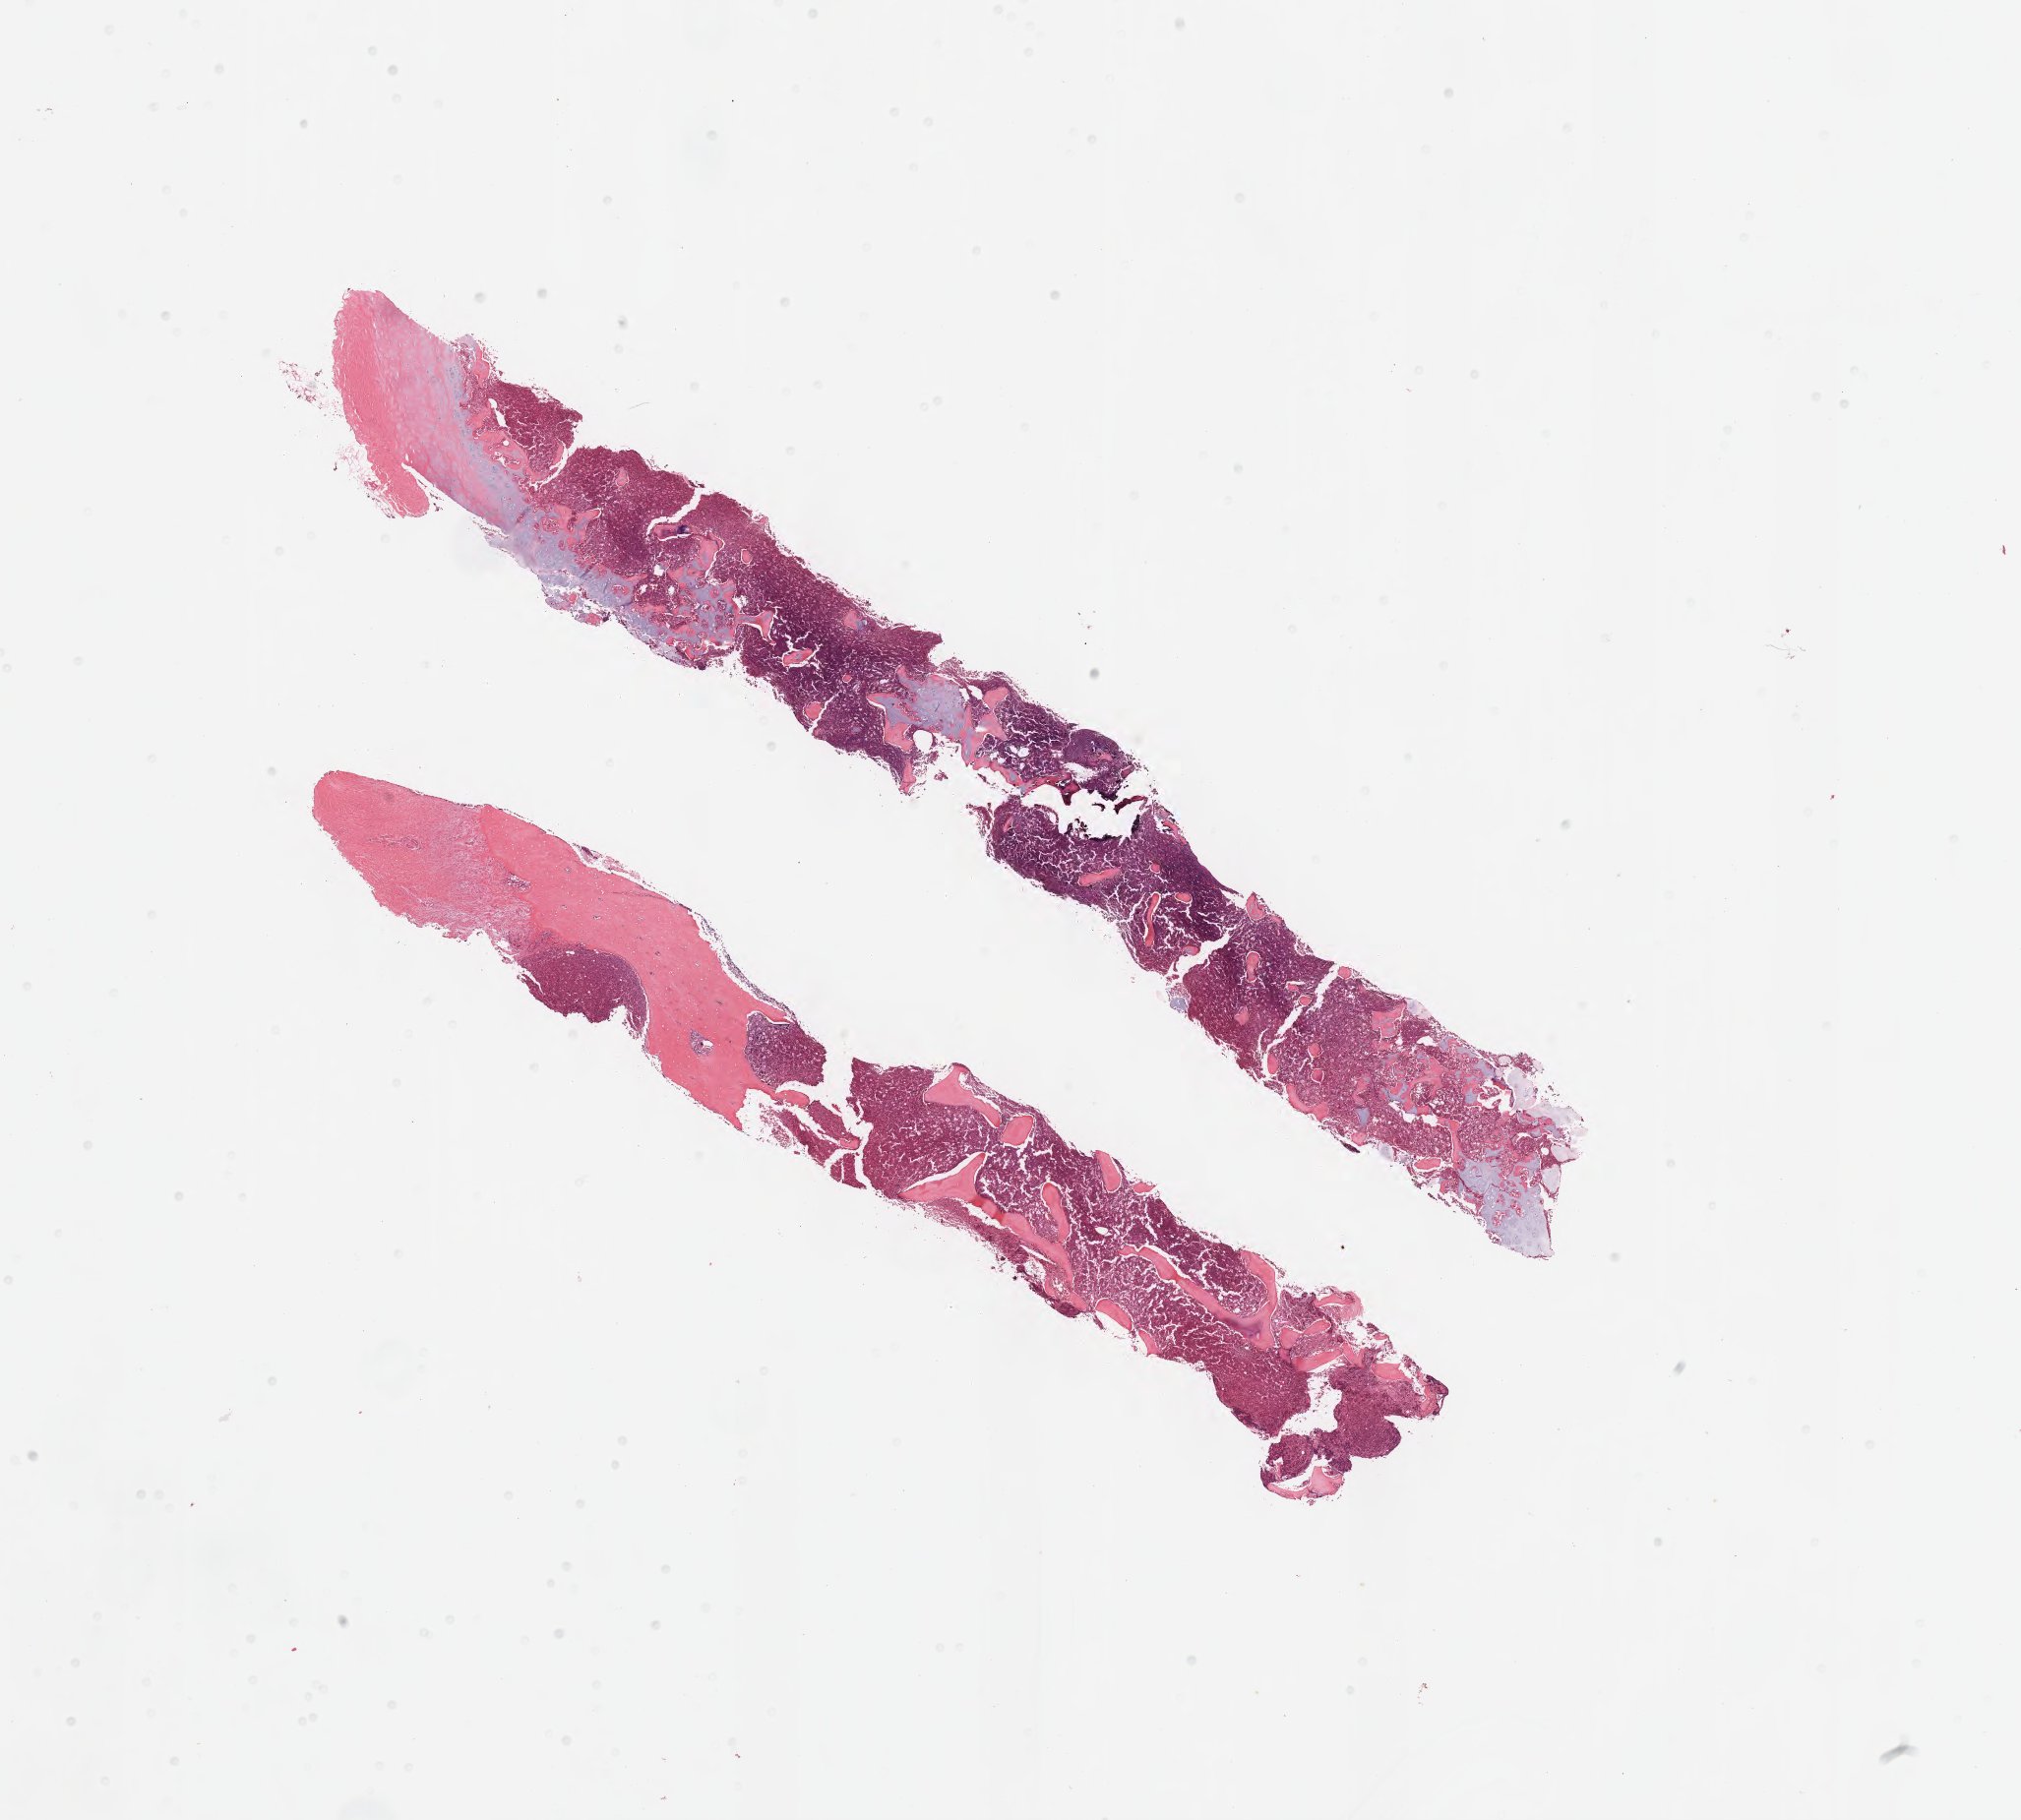
Hematoxylin and eosin (H&E) whole-slide image — whole scanned area (about 16.6 x 14.9 mm) shown as a low-resolution overview; specimen: tumor tissue; anatomic site: bone marrow. Patient: male, age 16 years.
Diagnosis: Burkitt lymphoma, NOS.